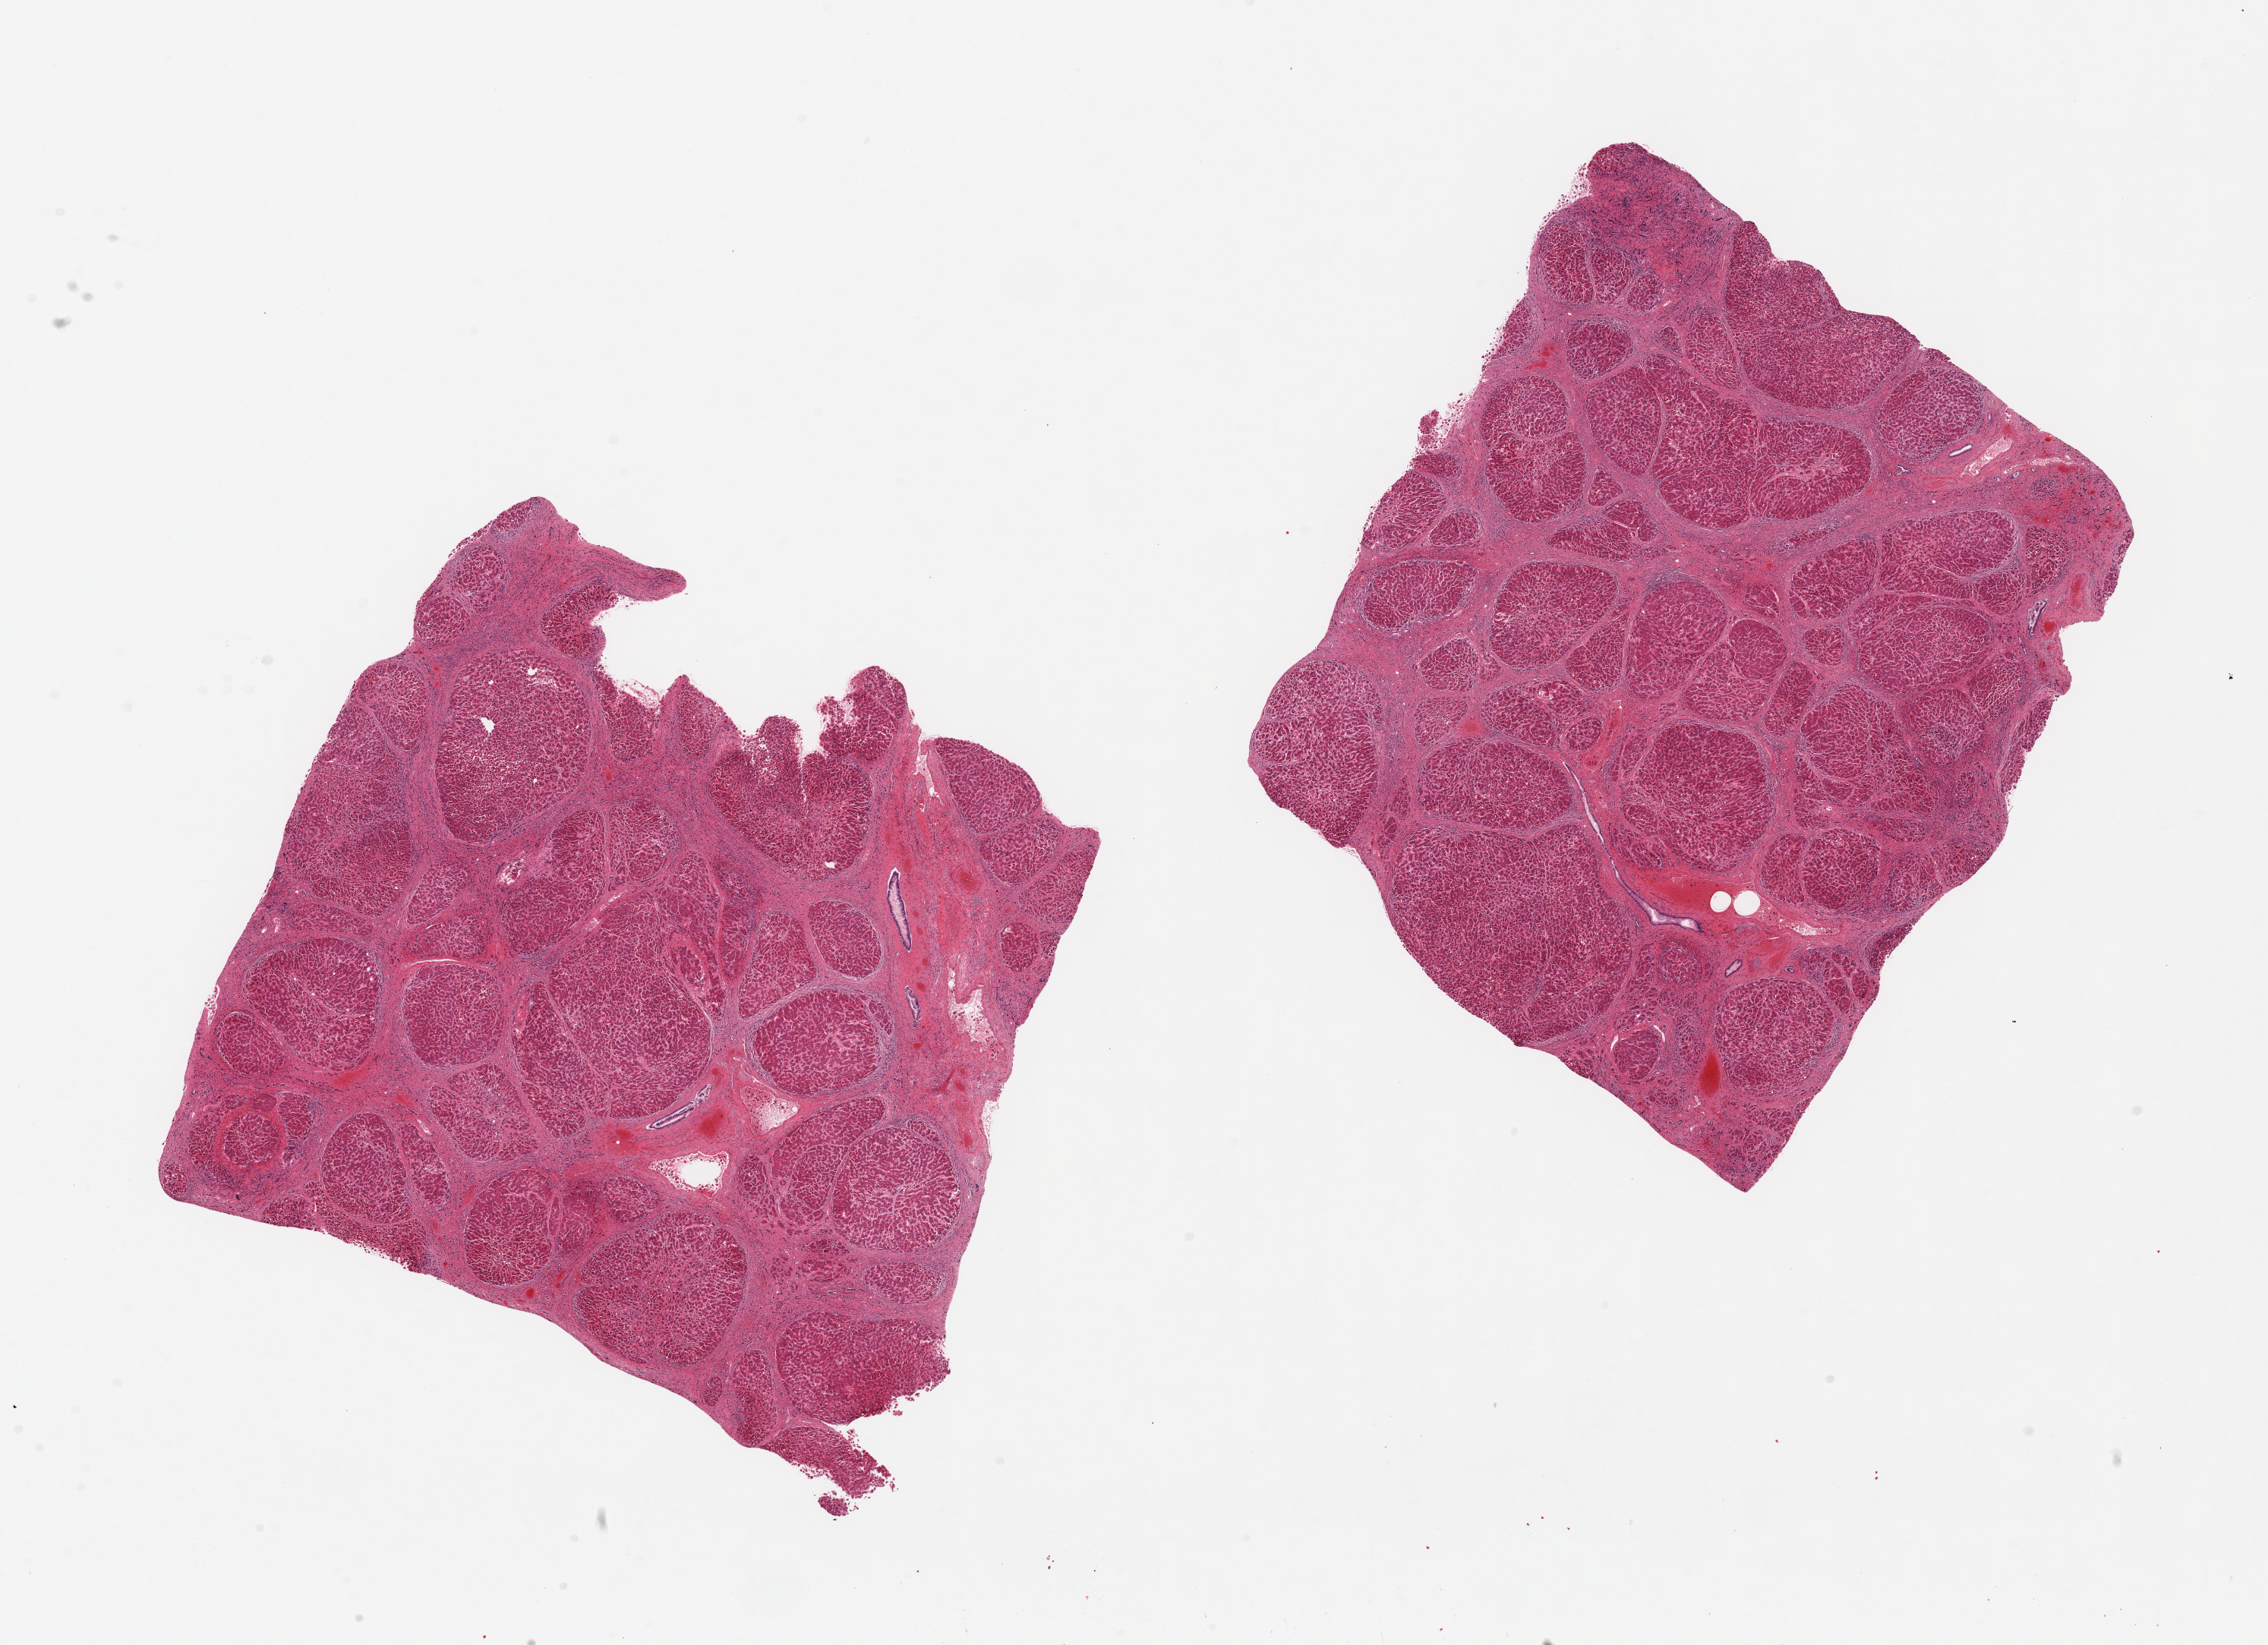
Digitized hematoxylin and eosin (H&E)-stained section, a low-resolution overview of the entire scanned area, about 23.6 x 17.1 mm. Donor: female.
Specimen: PAXgene-fixed, paraffin-embedded tissue; section of liver (target tissue); tissue donor sample.